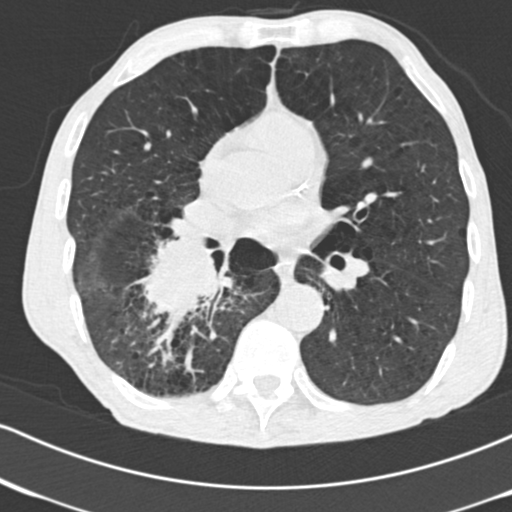
Low-dose screening chest CT, one axial slice. Slice 84 of 182 in the series (ordered by position). 120 kVp. Lung window (W 1500 / L -600 HU). 512 × 512 image matrix.
Outlined on this slice (outlined manually by an expert reader):
- lesion 1 (tumor, lower lobe of right lung): box from (x=144, y=242) to (x=223, y=319) px